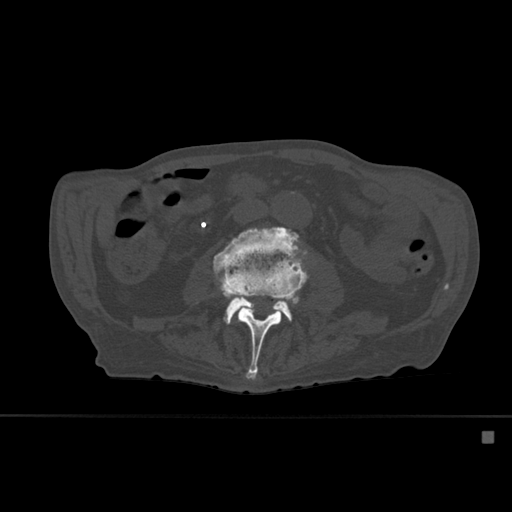
CT including the spine, one axial slice. Slice 208 of 527 in the series (ordered by position). Bone window (W 1800 / L 400 HU). 1.5 mm slice thickness. 512 × 512 image matrix, field of view 373 × 373 mm. Patient: male, 78 years. From the clinical record (not read from this slice): primary cancer: prostate.
Structures marked on this image (semi-automatically segmented with operator editing):
- L3 vertebra: box from (x=215, y=255) to (x=308, y=379) px
- L4 vertebra: (x=213, y=227)–(x=307, y=323)